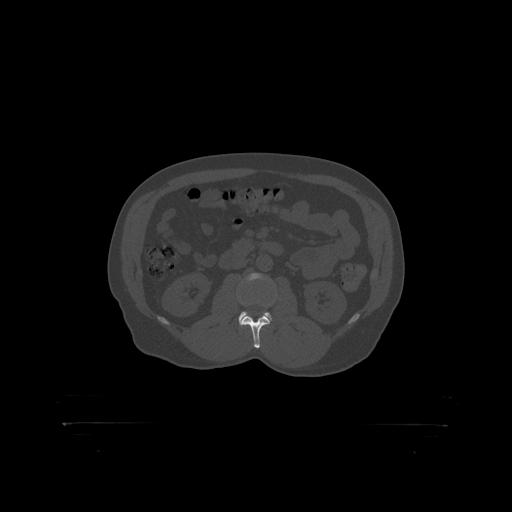
CT including the spine, one axial slice. Slice 284 of 399 in the series (ordered by position). Reconstruction kernel STANDARD. 120 kVp. Bone window (W 1800 / L 400 HU). 512 × 512 image matrix, field of view 650 × 650 mm. Male patient, age 46 years. From the clinical record (not read from this slice): primary cancer: skin.
Annotated regions visible in this slice (semi-automatically segmented with operator editing):
- L2 vertebra: bounding box (x1, y1, x2, y2) in pixels: (244, 305, 270, 319)
- L3 vertebra: (240, 274, 272, 318)